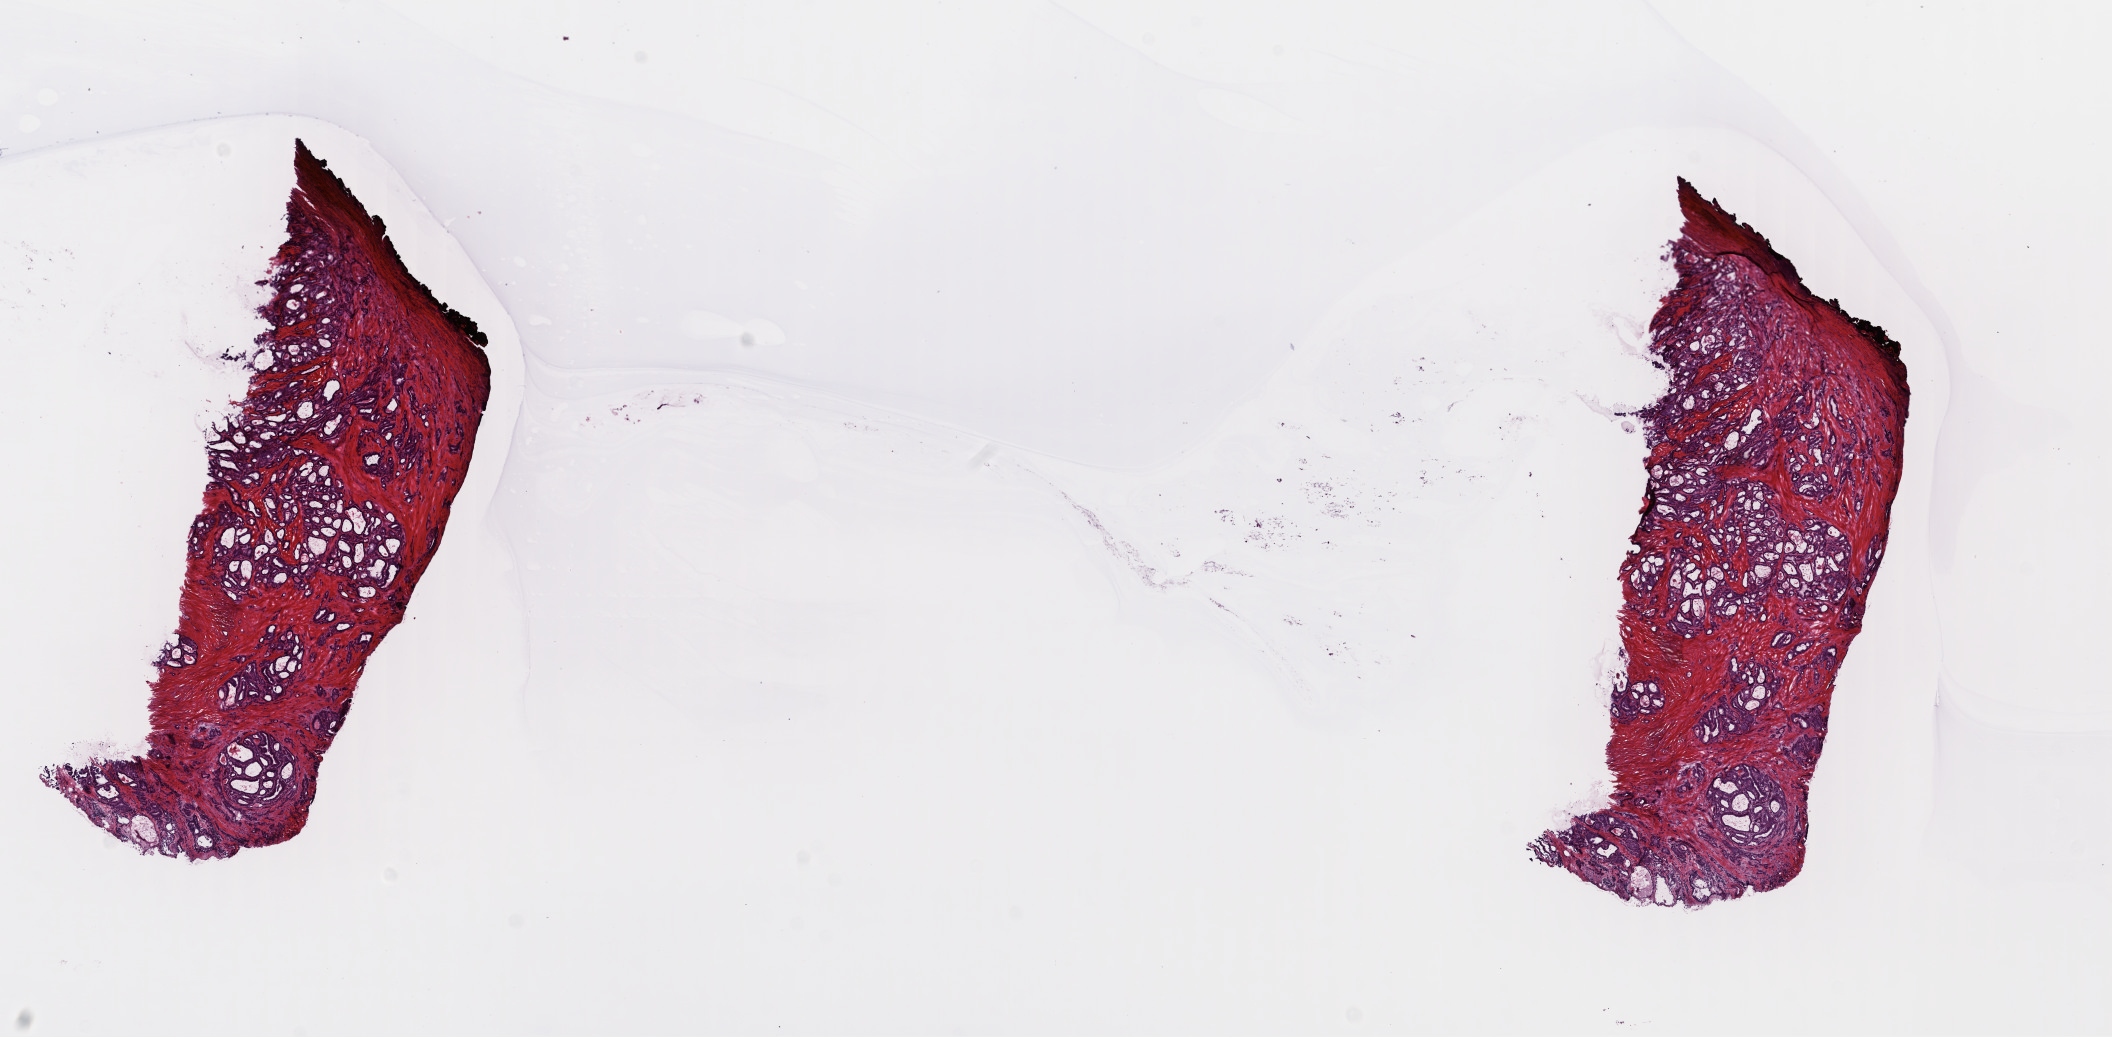
Digitized Hematoxylin and eosin (H&E) stained tissue section (whole slide), a low-resolution overview of the entire scanned area, about 16.6 x 8.2 mm (acquisition: 40x scan). Frozen section from the top of the tissue portion. Primary tumour sample from the thyroid. Patient: male, age at initial diagnosis 45 years. Pathologist review of this section (percent, as recorded): tumour cells 40%, tumour nuclei 100%, normal cells 0%, stromal cells 60%, necrosis 0%. Inflammatory infiltration, as recorded: lymphocyte infiltration 2%, monocyte infiltration 1%, neutrophil infiltration 0%.
AJCC pathologic stage: III (7th edition). Lymph nodes positive (case pathology): 1 of 1 examined. Diagnosis: Papillary adenocarcinoma, NOS (thyroid gland). TNM: T1b N1a MX.